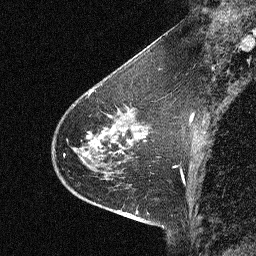
Breast MRI (dynamic contrast-enhanced), one sagittal slice; dynamic contrast-enhanced study with each time point stored as its own series, time point 2 of 3 at this slice position (early post-contrast, ordered by acquisition time); 1.5 T; TE 4.5 ms, TR 11 ms; 2.06 mm slice thickness; 256 × 256 image matrix, field of view 200 × 200 mm. Patient: female, 46 years. From the clinical record (not read from this slice): setting: breast cancer imaged before/during neoadjuvant chemotherapy; receptor status: HER2-positive.
Annotated regions visible in this slice (semi-automatically segmented with operator editing):
- analysis volume of interest (the breast-tissue region the enhancement analysis was run in; not a lesion): bounding box <42,80,150,180> (left, top, right, bottom; pixels)
- tumour enhancement mask (voxels above the 90 % enhancement threshold inside the analysis volume of interest): <73,109,129,162>